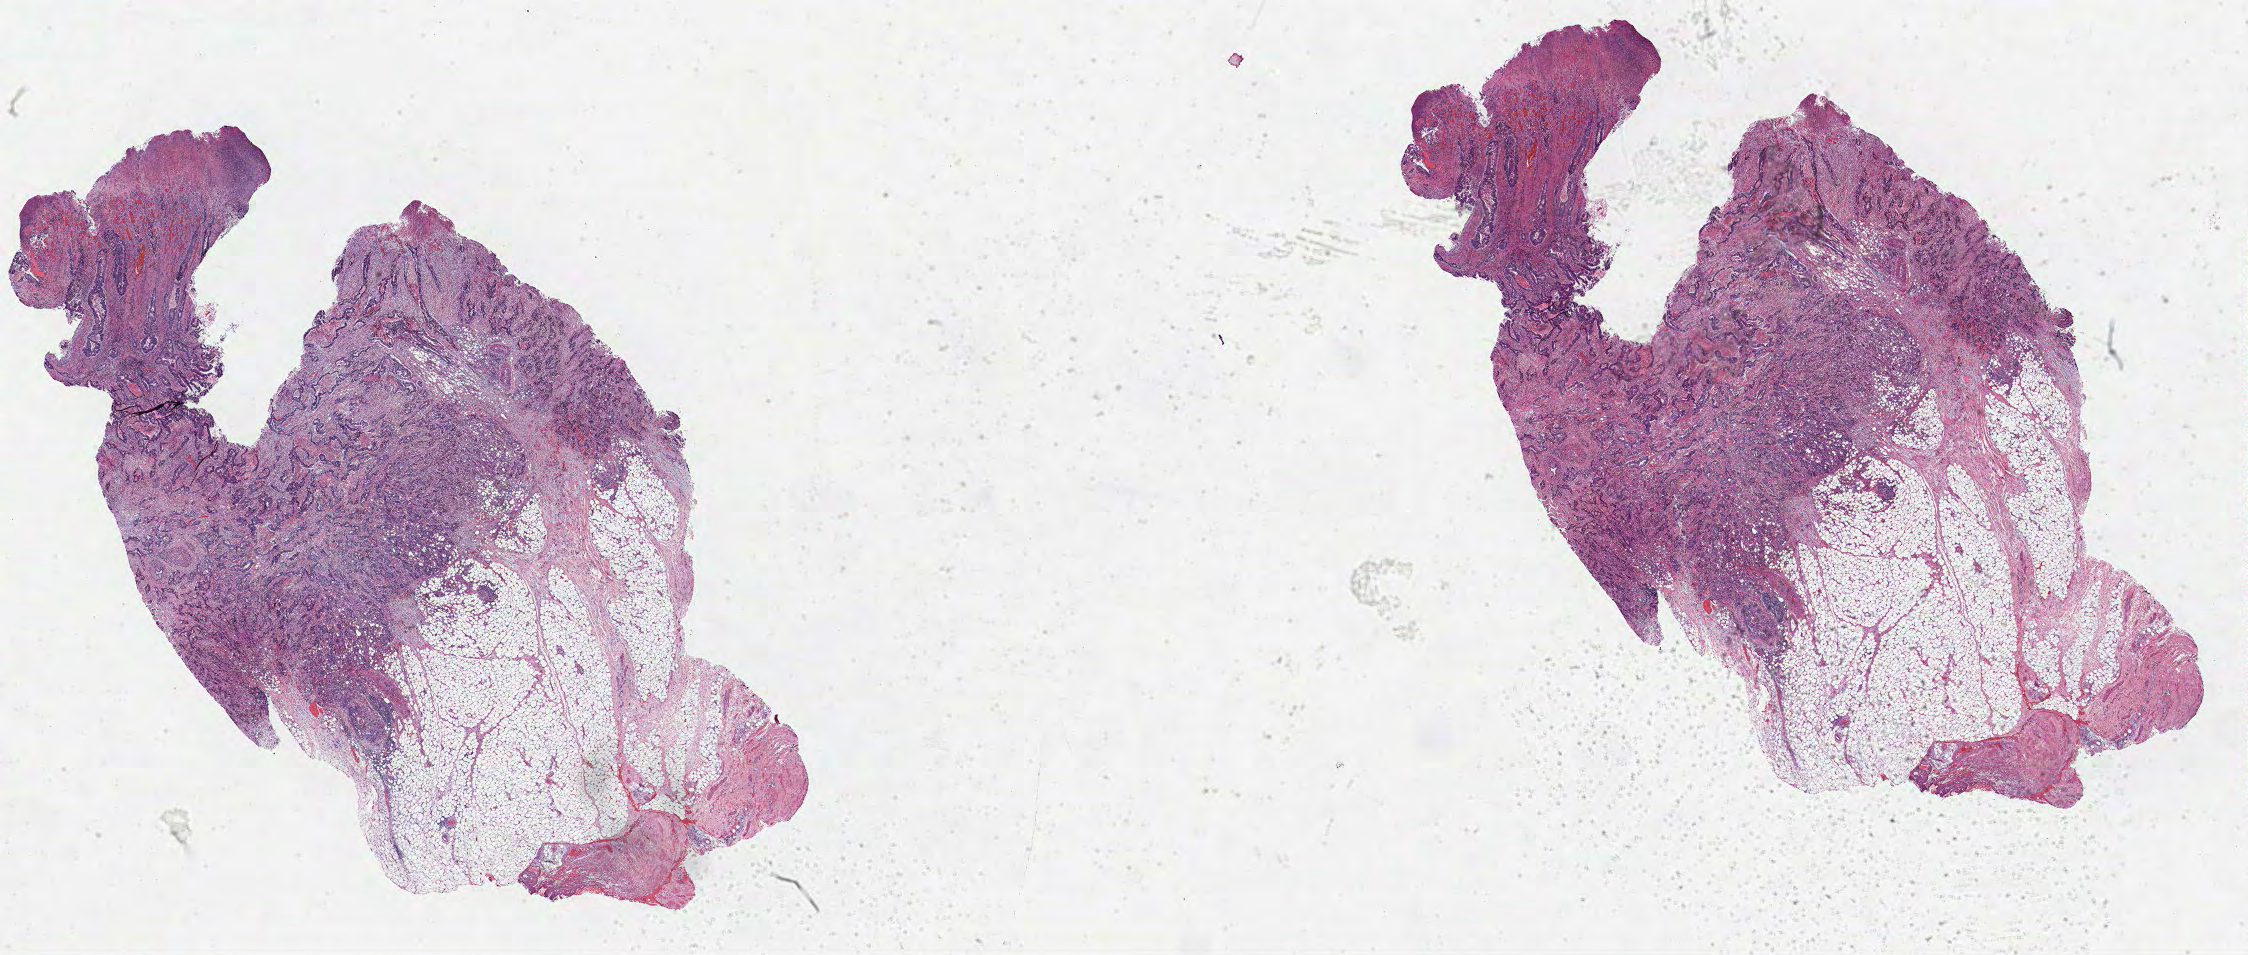
Hematoxylin and eosin (H&E) stained whole-slide image — a low-resolution overview of the entire scanned area, about 36.3 x 15.4 mm. FFPE section. Sample: primary tumour, rectum. Male, age 39 years at initial diagnosis.
Pathologic diagnosis: Adenocarcinoma, NOS (rectosigmoid junction).